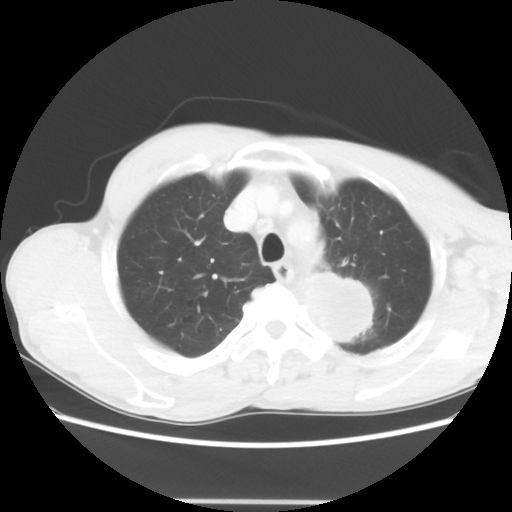
Chest CT, one axial slice. Slice 52 of 62 in the series (ordered by position). Reconstruction kernel STANDARD. 100 kVp. Lung window (W 1500 / L -600 HU). 512 × 512 image matrix, field of view 360 × 360 mm. Male patient, age 61 years. From the clinical record (not read from this slice): clinical TNM (as recorded): T3 N1 M1.
Structures marked on this image (rectangle marked by the reading radiologist):
- lung tumour (recorded histology: adenocarcinoma): box from (x=309, y=262) to (x=396, y=359) px